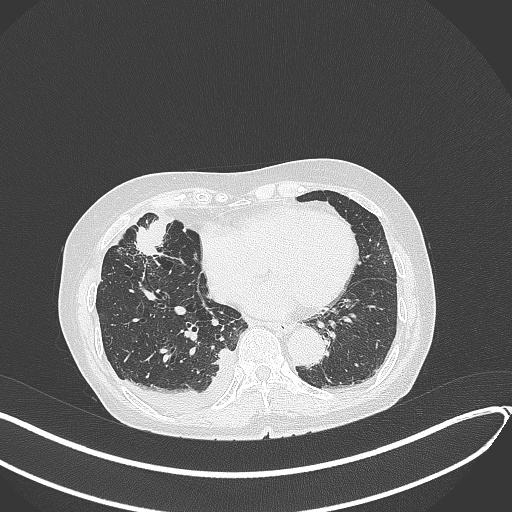
Chest CT, one axial slice. Slice 133 of 418 in the series (ordered by position). Reconstruction kernel B70f. 120 kVp. Lung window (W 1500 / L -600 HU). 512 × 512 image matrix, field of view 400 × 400 mm. Patient: female, 75 years. Case-level facts recorded for this patient, not image findings: clinical TNM (as recorded): T2a N3 M0.
Structures marked on this image (rectangle marked by the reading radiologist):
- lung tumour (recorded histology: adenocarcinoma): bounding box <130,217,172,260> (left, top, right, bottom; pixels)